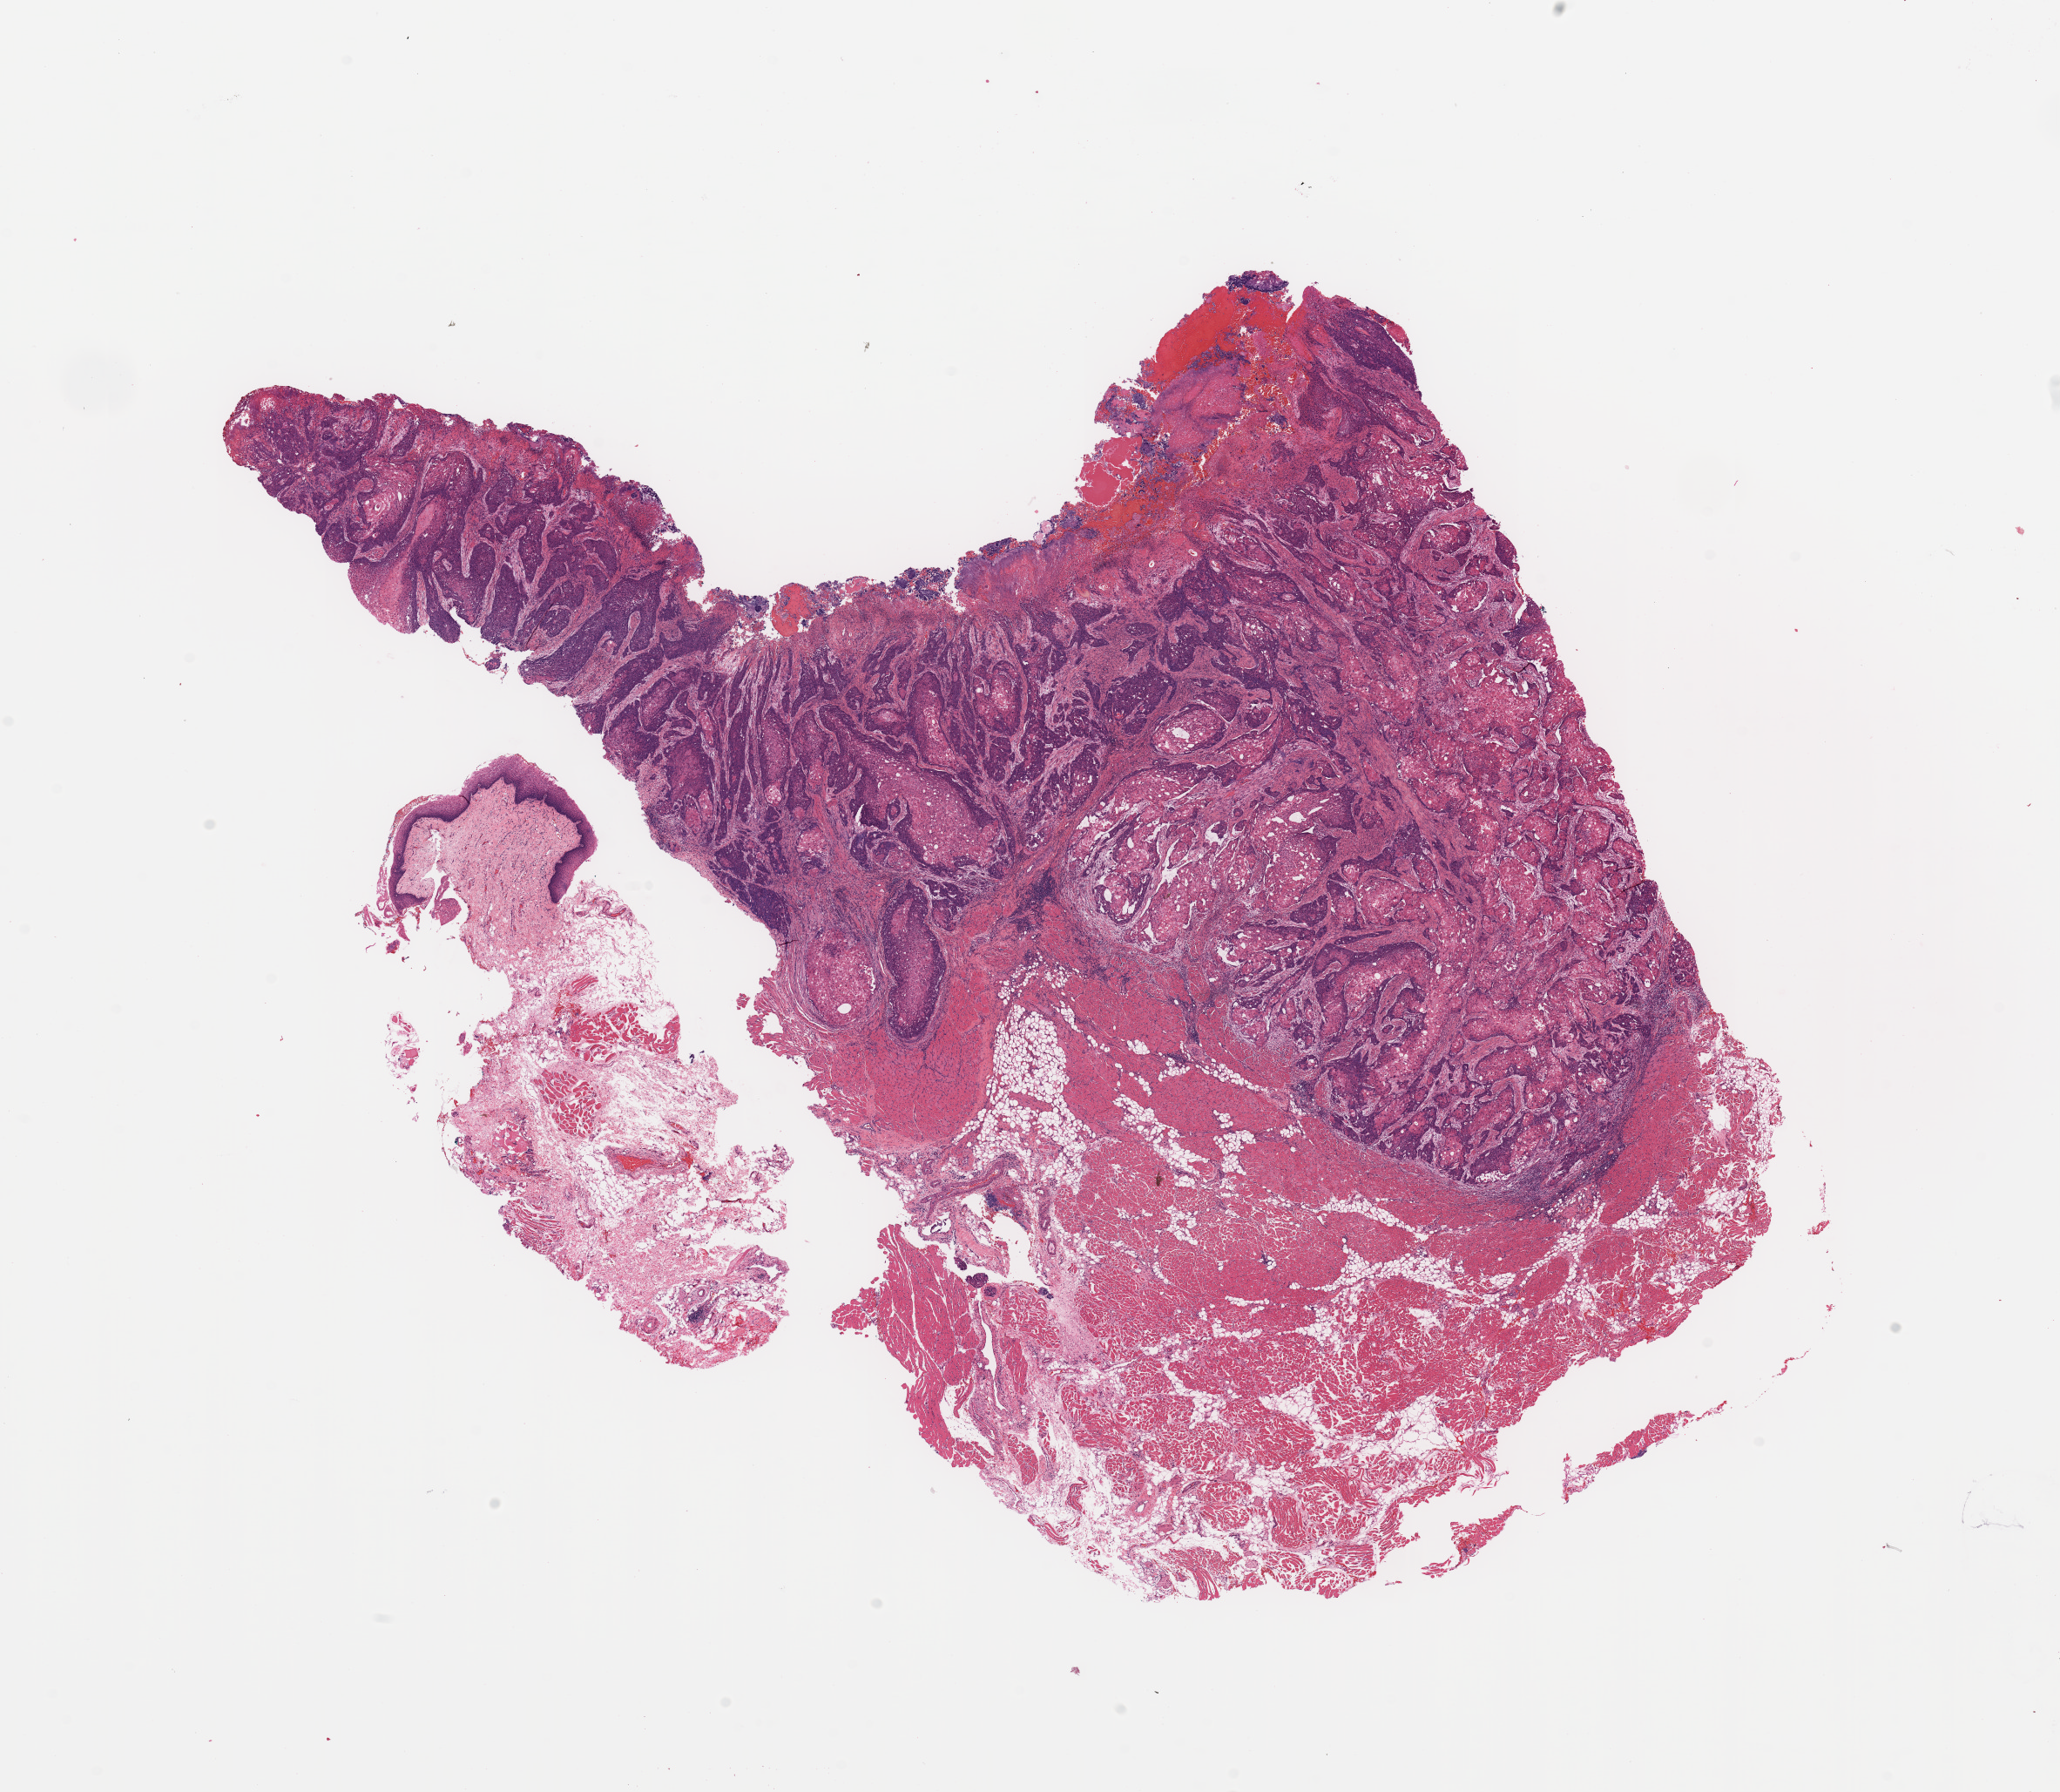
Digitized H&E-stained tissue section (whole slide) — low-resolution overview of the scanned area, about 18.7 x 16.3 mm (slide scanned at 20x). Head and neck, tissue type not recorded. Male, 61 y/o.
Patient diagnosis: Squamous cell carcinoma, NOS (tongue, NOS).